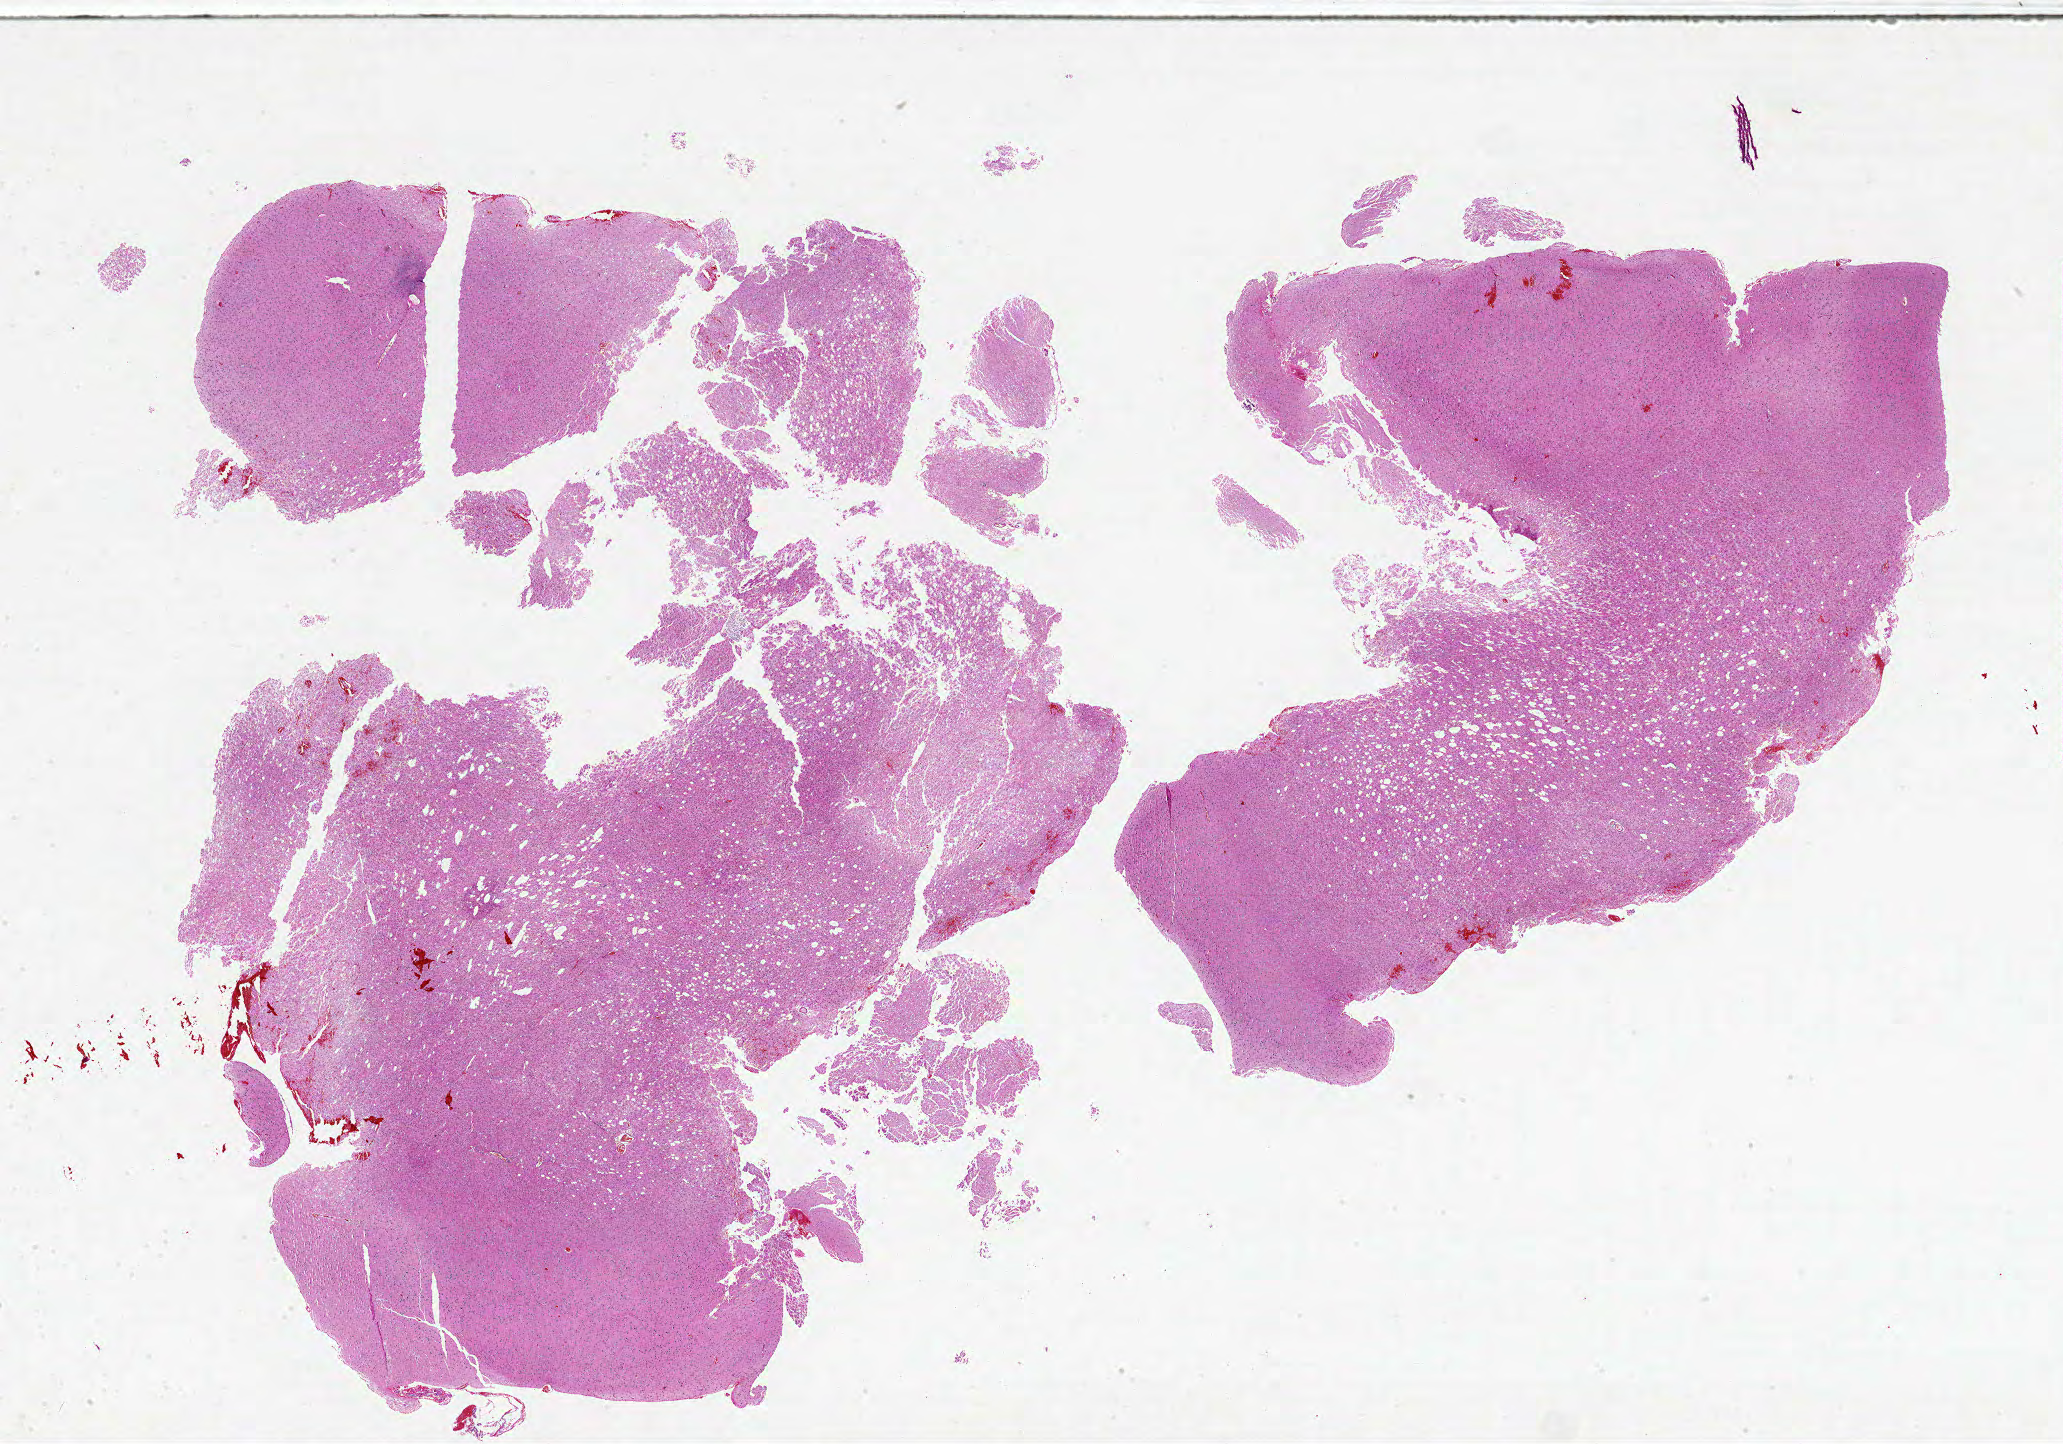
H&E-stained whole-slide image, shown as a low-resolution overview of the whole scanned area (about 33.0 x 23.1 mm); formalin-fixed paraffin-embedded (FFPE) diagnostic section; primary tumour sample from the brain. Male, age 76 years at initial diagnosis.
* diagnosis: Glioblastoma